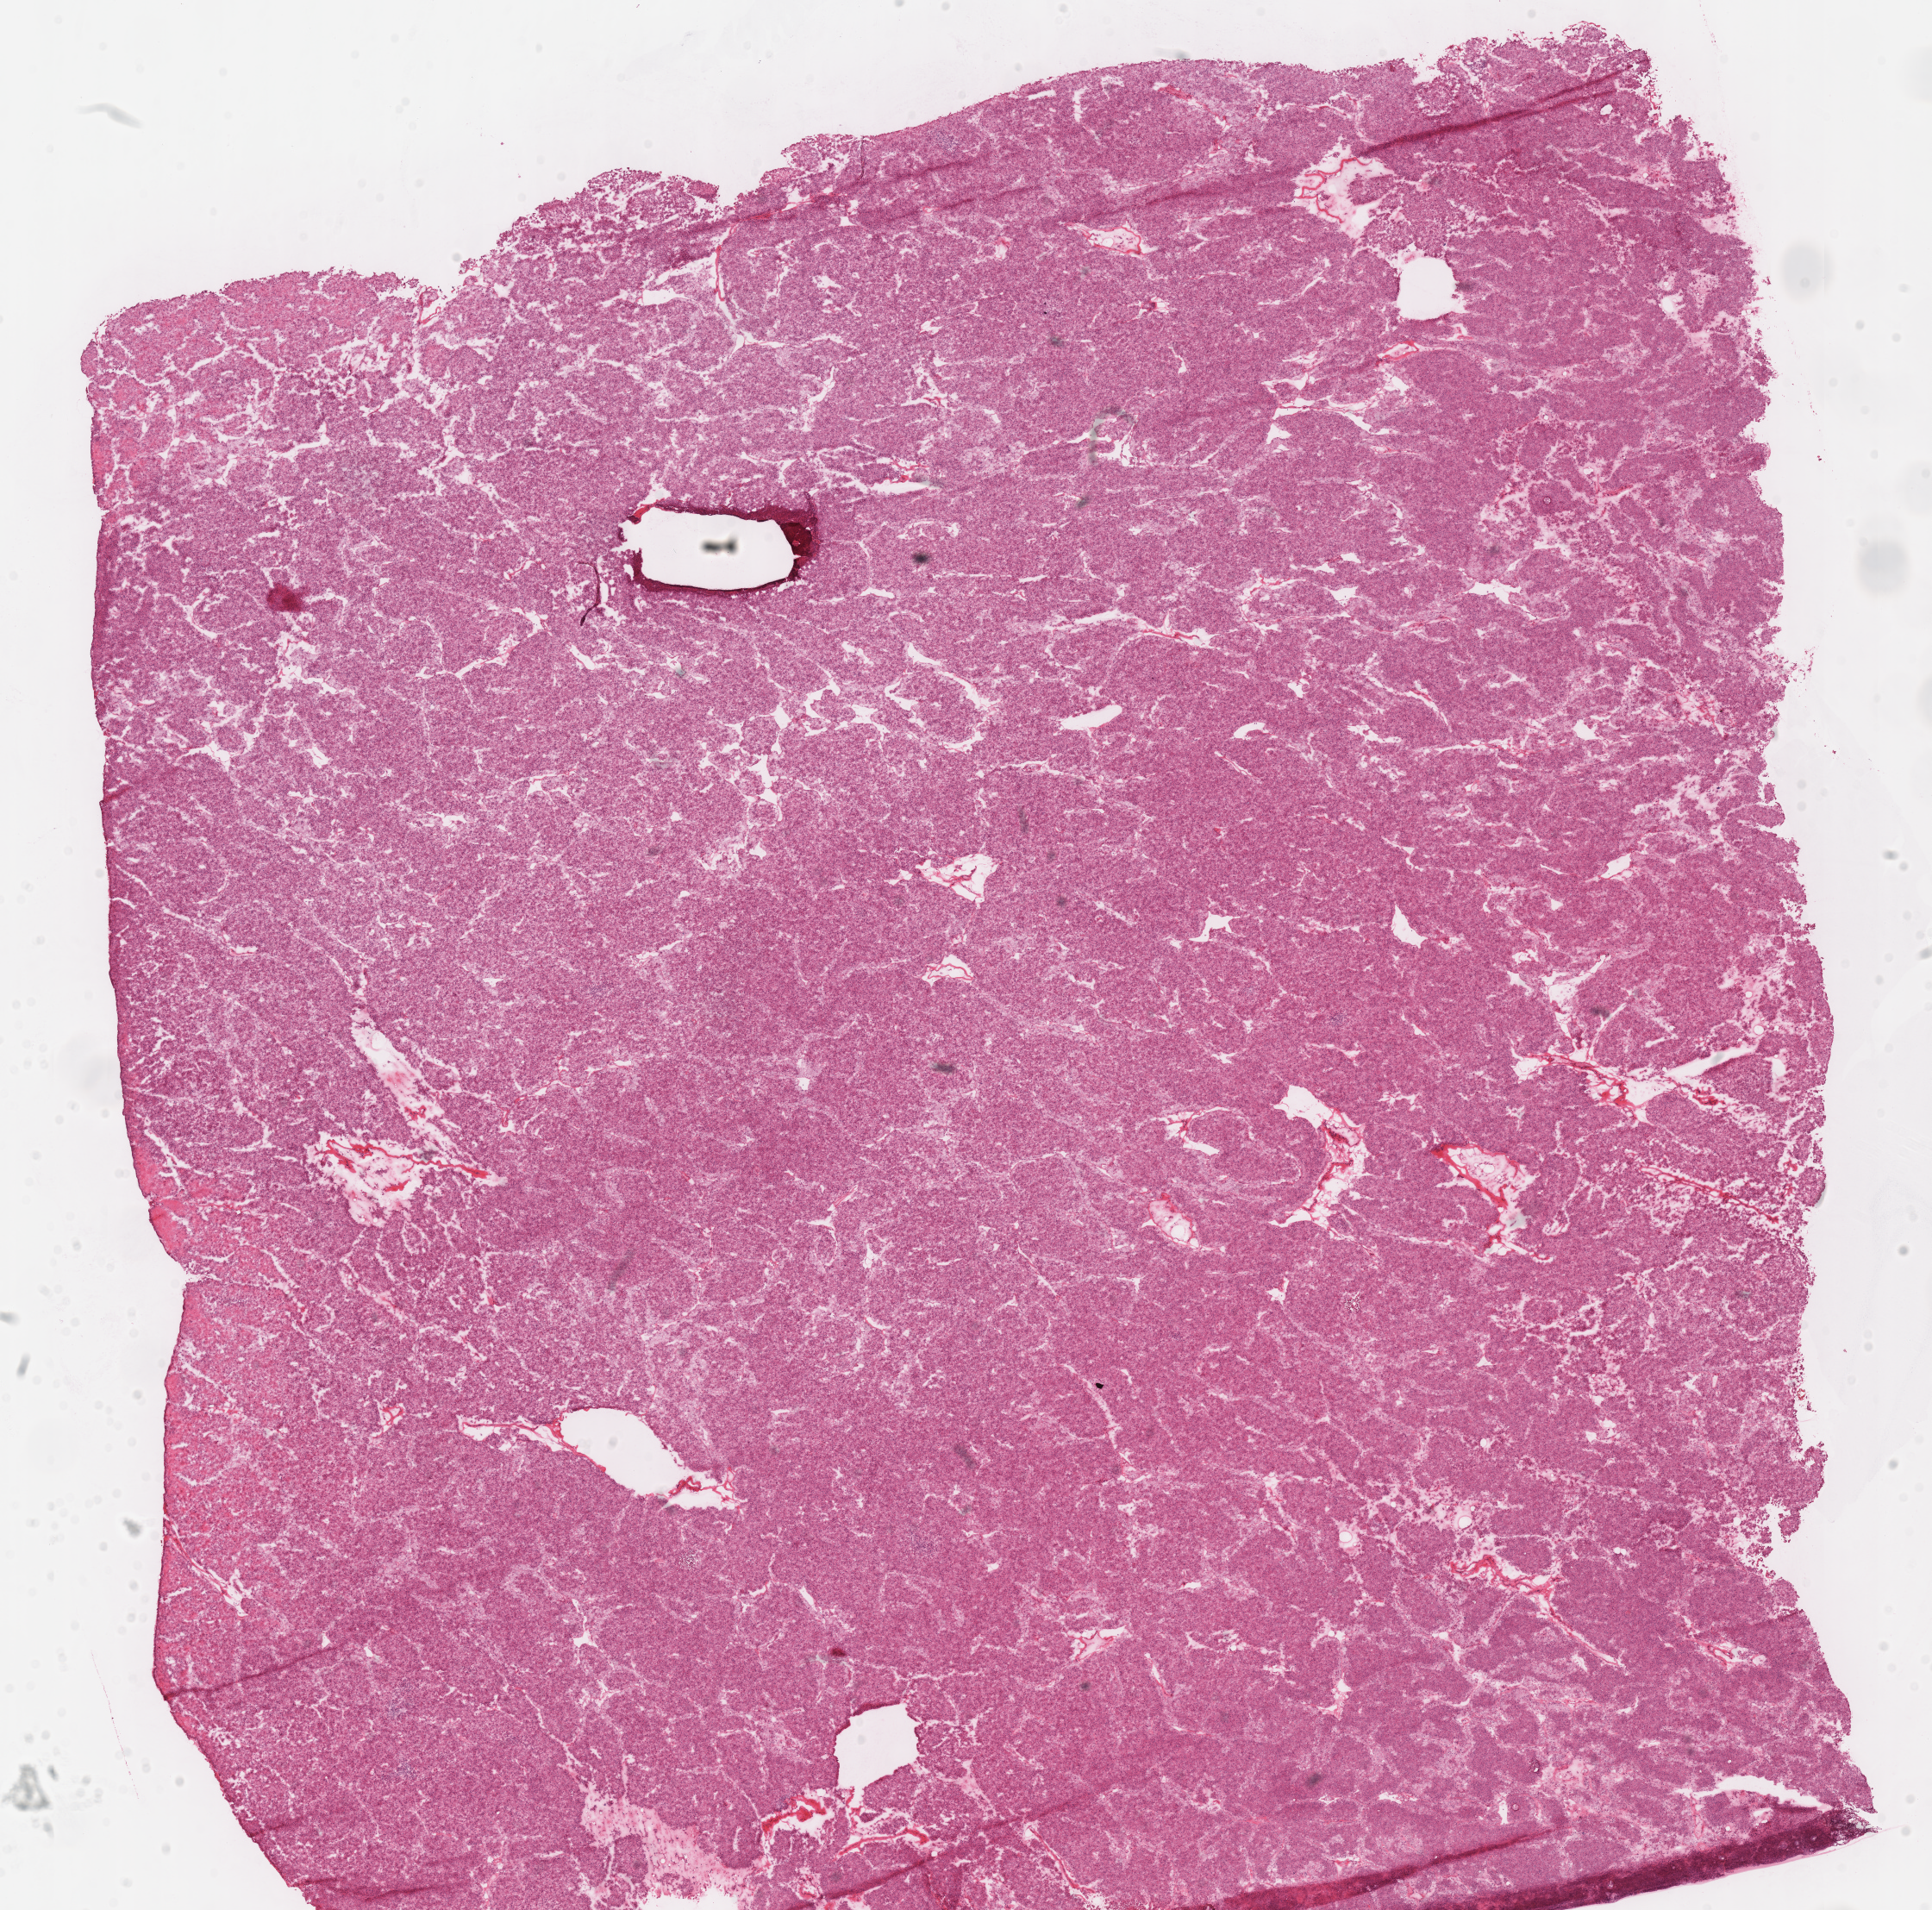
Whole-slide histology image, H&E, a low-resolution overview of the entire scanned area, about 17.6 x 17.4 mm (slide scanned at 40x), frozen section from the top of the tissue portion, kidney, primary tumour sample. Patient: female, age at initial diagnosis 56 years. Composition of this section per pathologist review: tumour cells 100%, tumour nuclei 90%, normal cells 0%, stromal cells 0%, necrosis 0%. Inflammatory infiltration, as recorded: lymphocyte infiltration 2%, monocyte infiltration 0%, neutrophil infiltration 0%.
AJCC pathologic stage: II (5th edition). Laterality: left. Pathologic diagnosis: Renal cell carcinoma, chromophobe type.